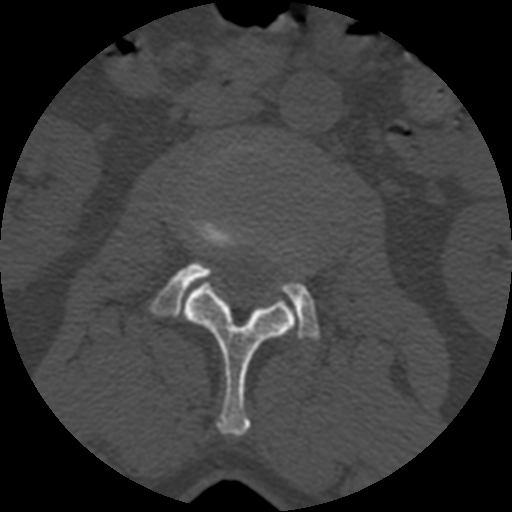
CT including the spine, one axial slice. Position 323 of 399 along the scan axis. Reconstruction kernel STANDARD. 120 kVp. Bone window (W 1800 / L 400 HU). 1.25 mm slice thickness. 512 × 512 image matrix, field of view 160 × 160 mm. Patient age 71 years. From the clinical record (not read from this slice): primary cancer: prostate.
Outlined on this slice (semi-automatic segmentation, software-assisted and operator-edited):
- L2 vertebra: bounding box [x1, y1, x2, y2] px = [175, 283, 295, 436]
- L3 vertebra: [147, 218, 320, 341]